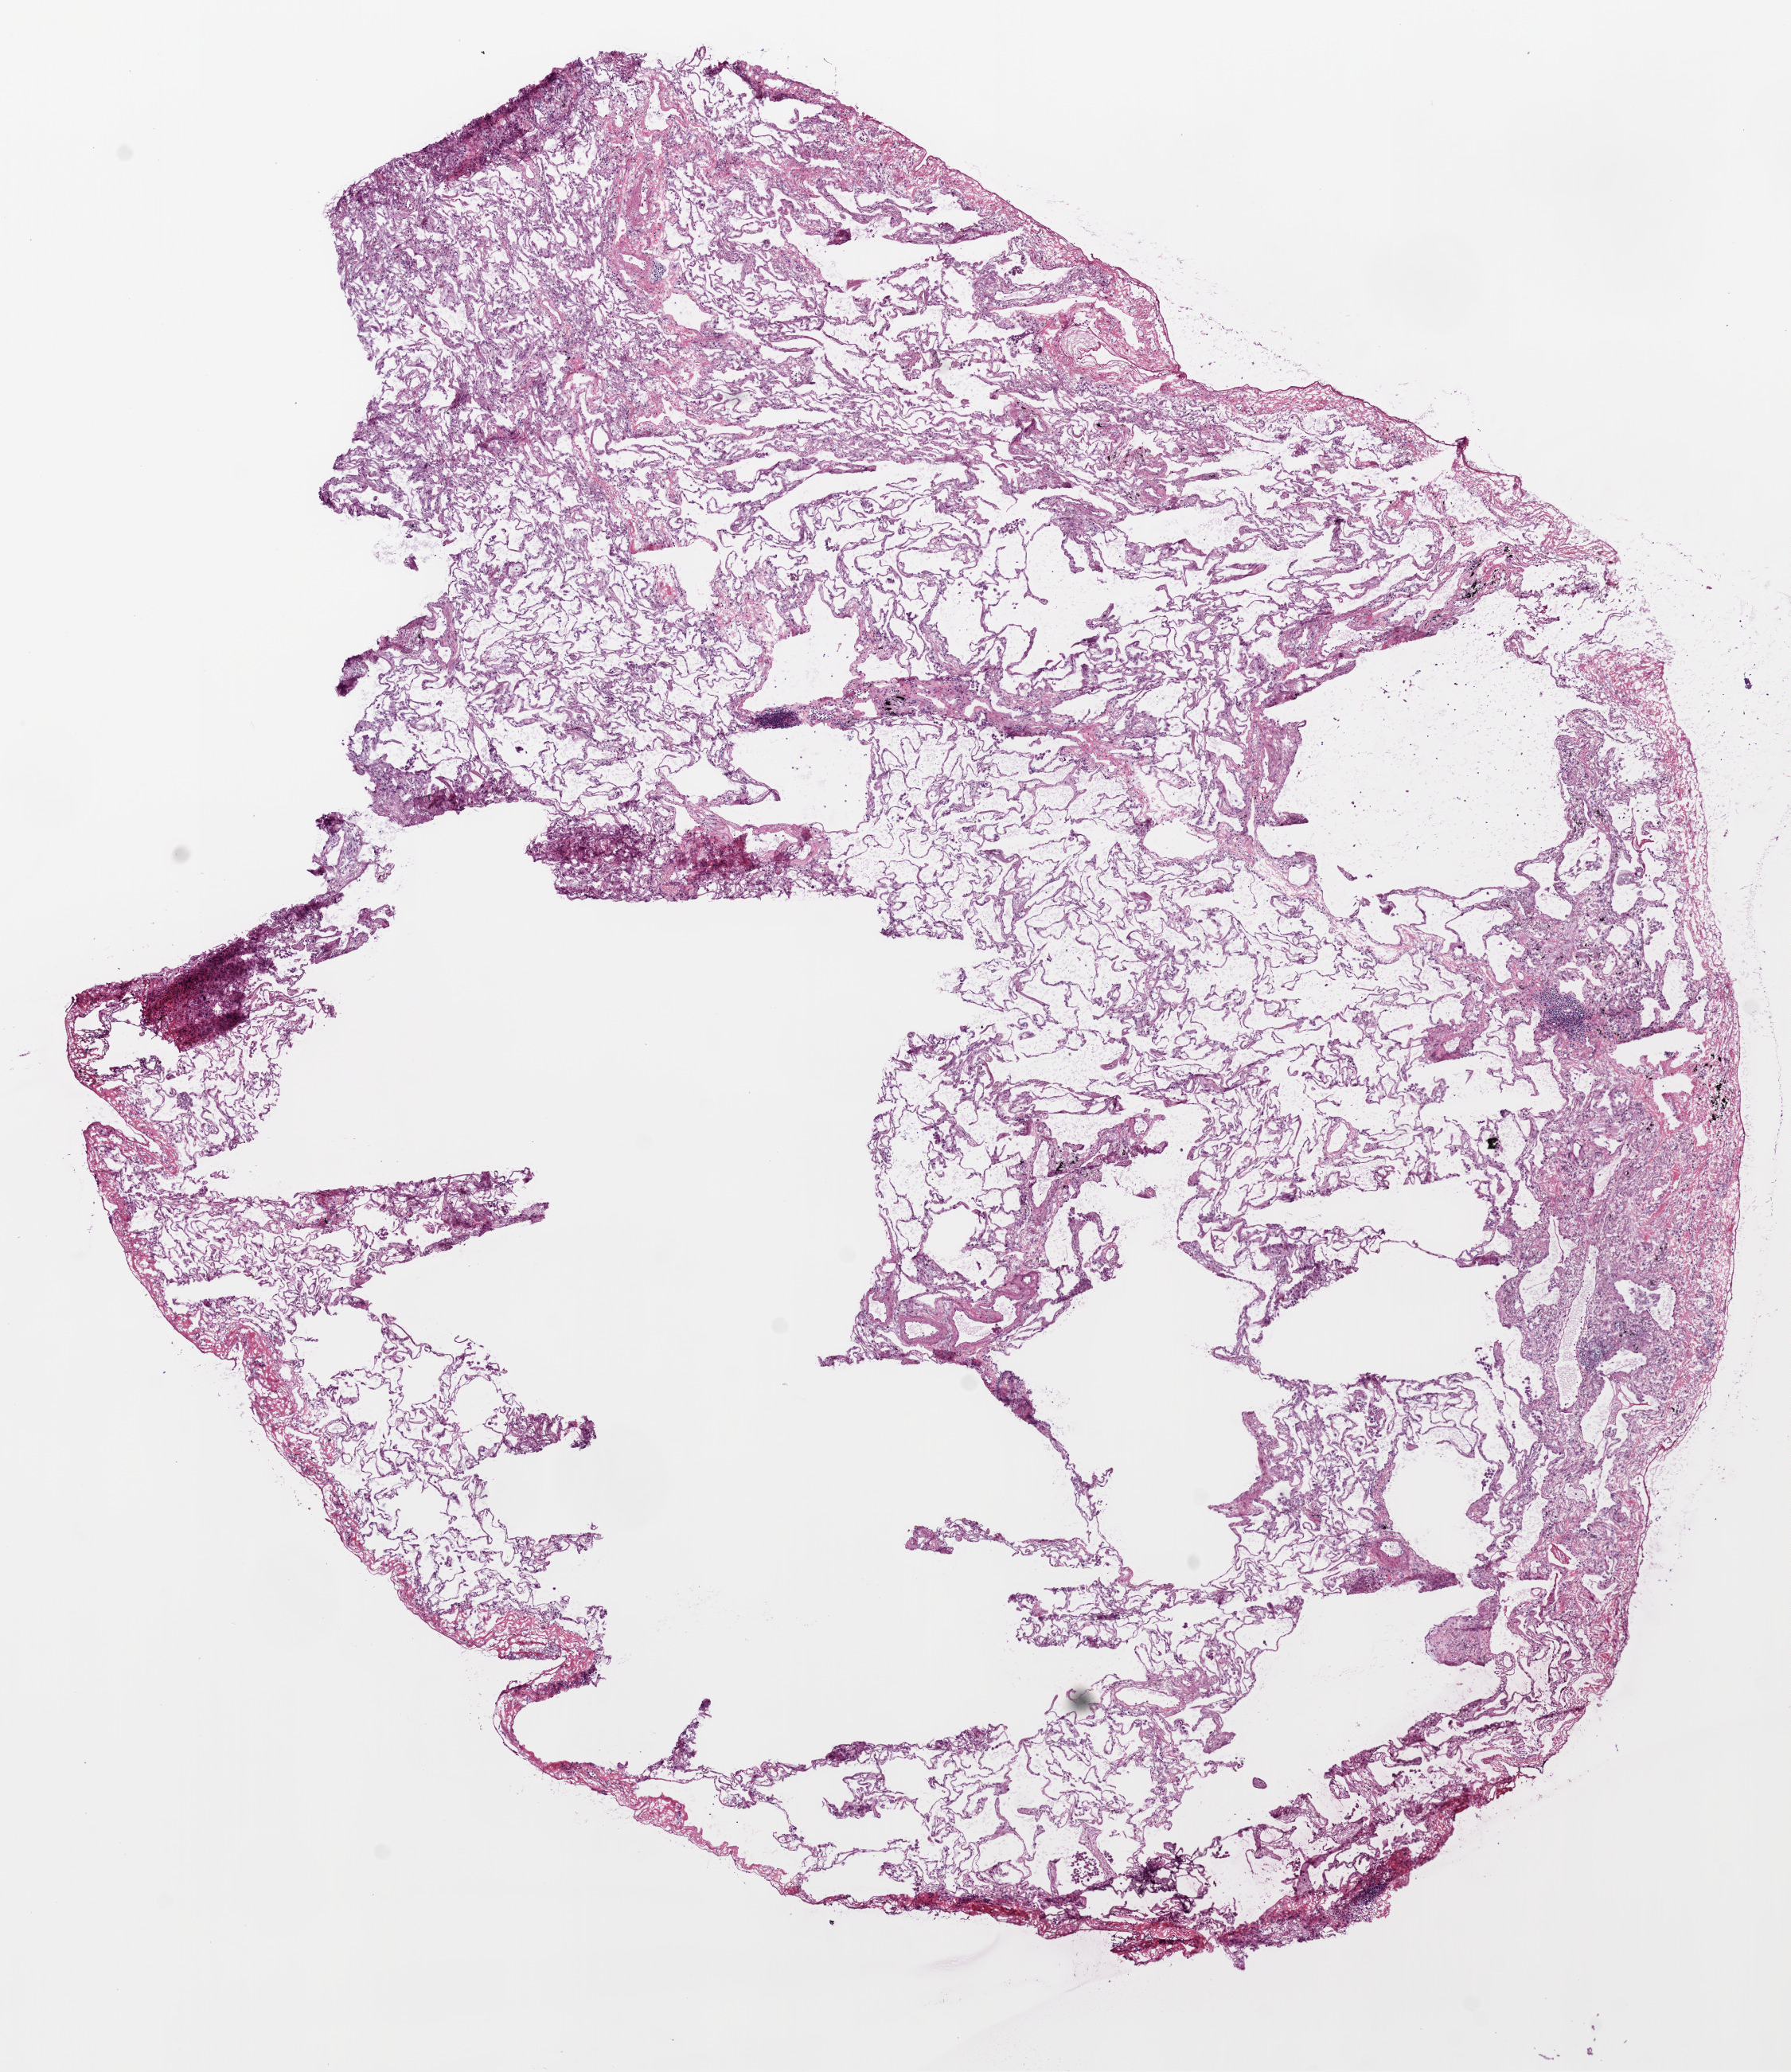
Whole-slide histology image, H&E, low-resolution overview of the scanned area, about 9.0 x 10.4 mm (slide scanned at 20x); frozen section from the bottom of the tissue portion; sample: solid tissue normal (non-tumour tissue), lung. Patient: female, age at initial diagnosis 73 years.
This section: solid tissue normal sample (biorepository sample class). Patient diagnosis: Squamous cell carcinoma, NOS (upper lobe, lung).